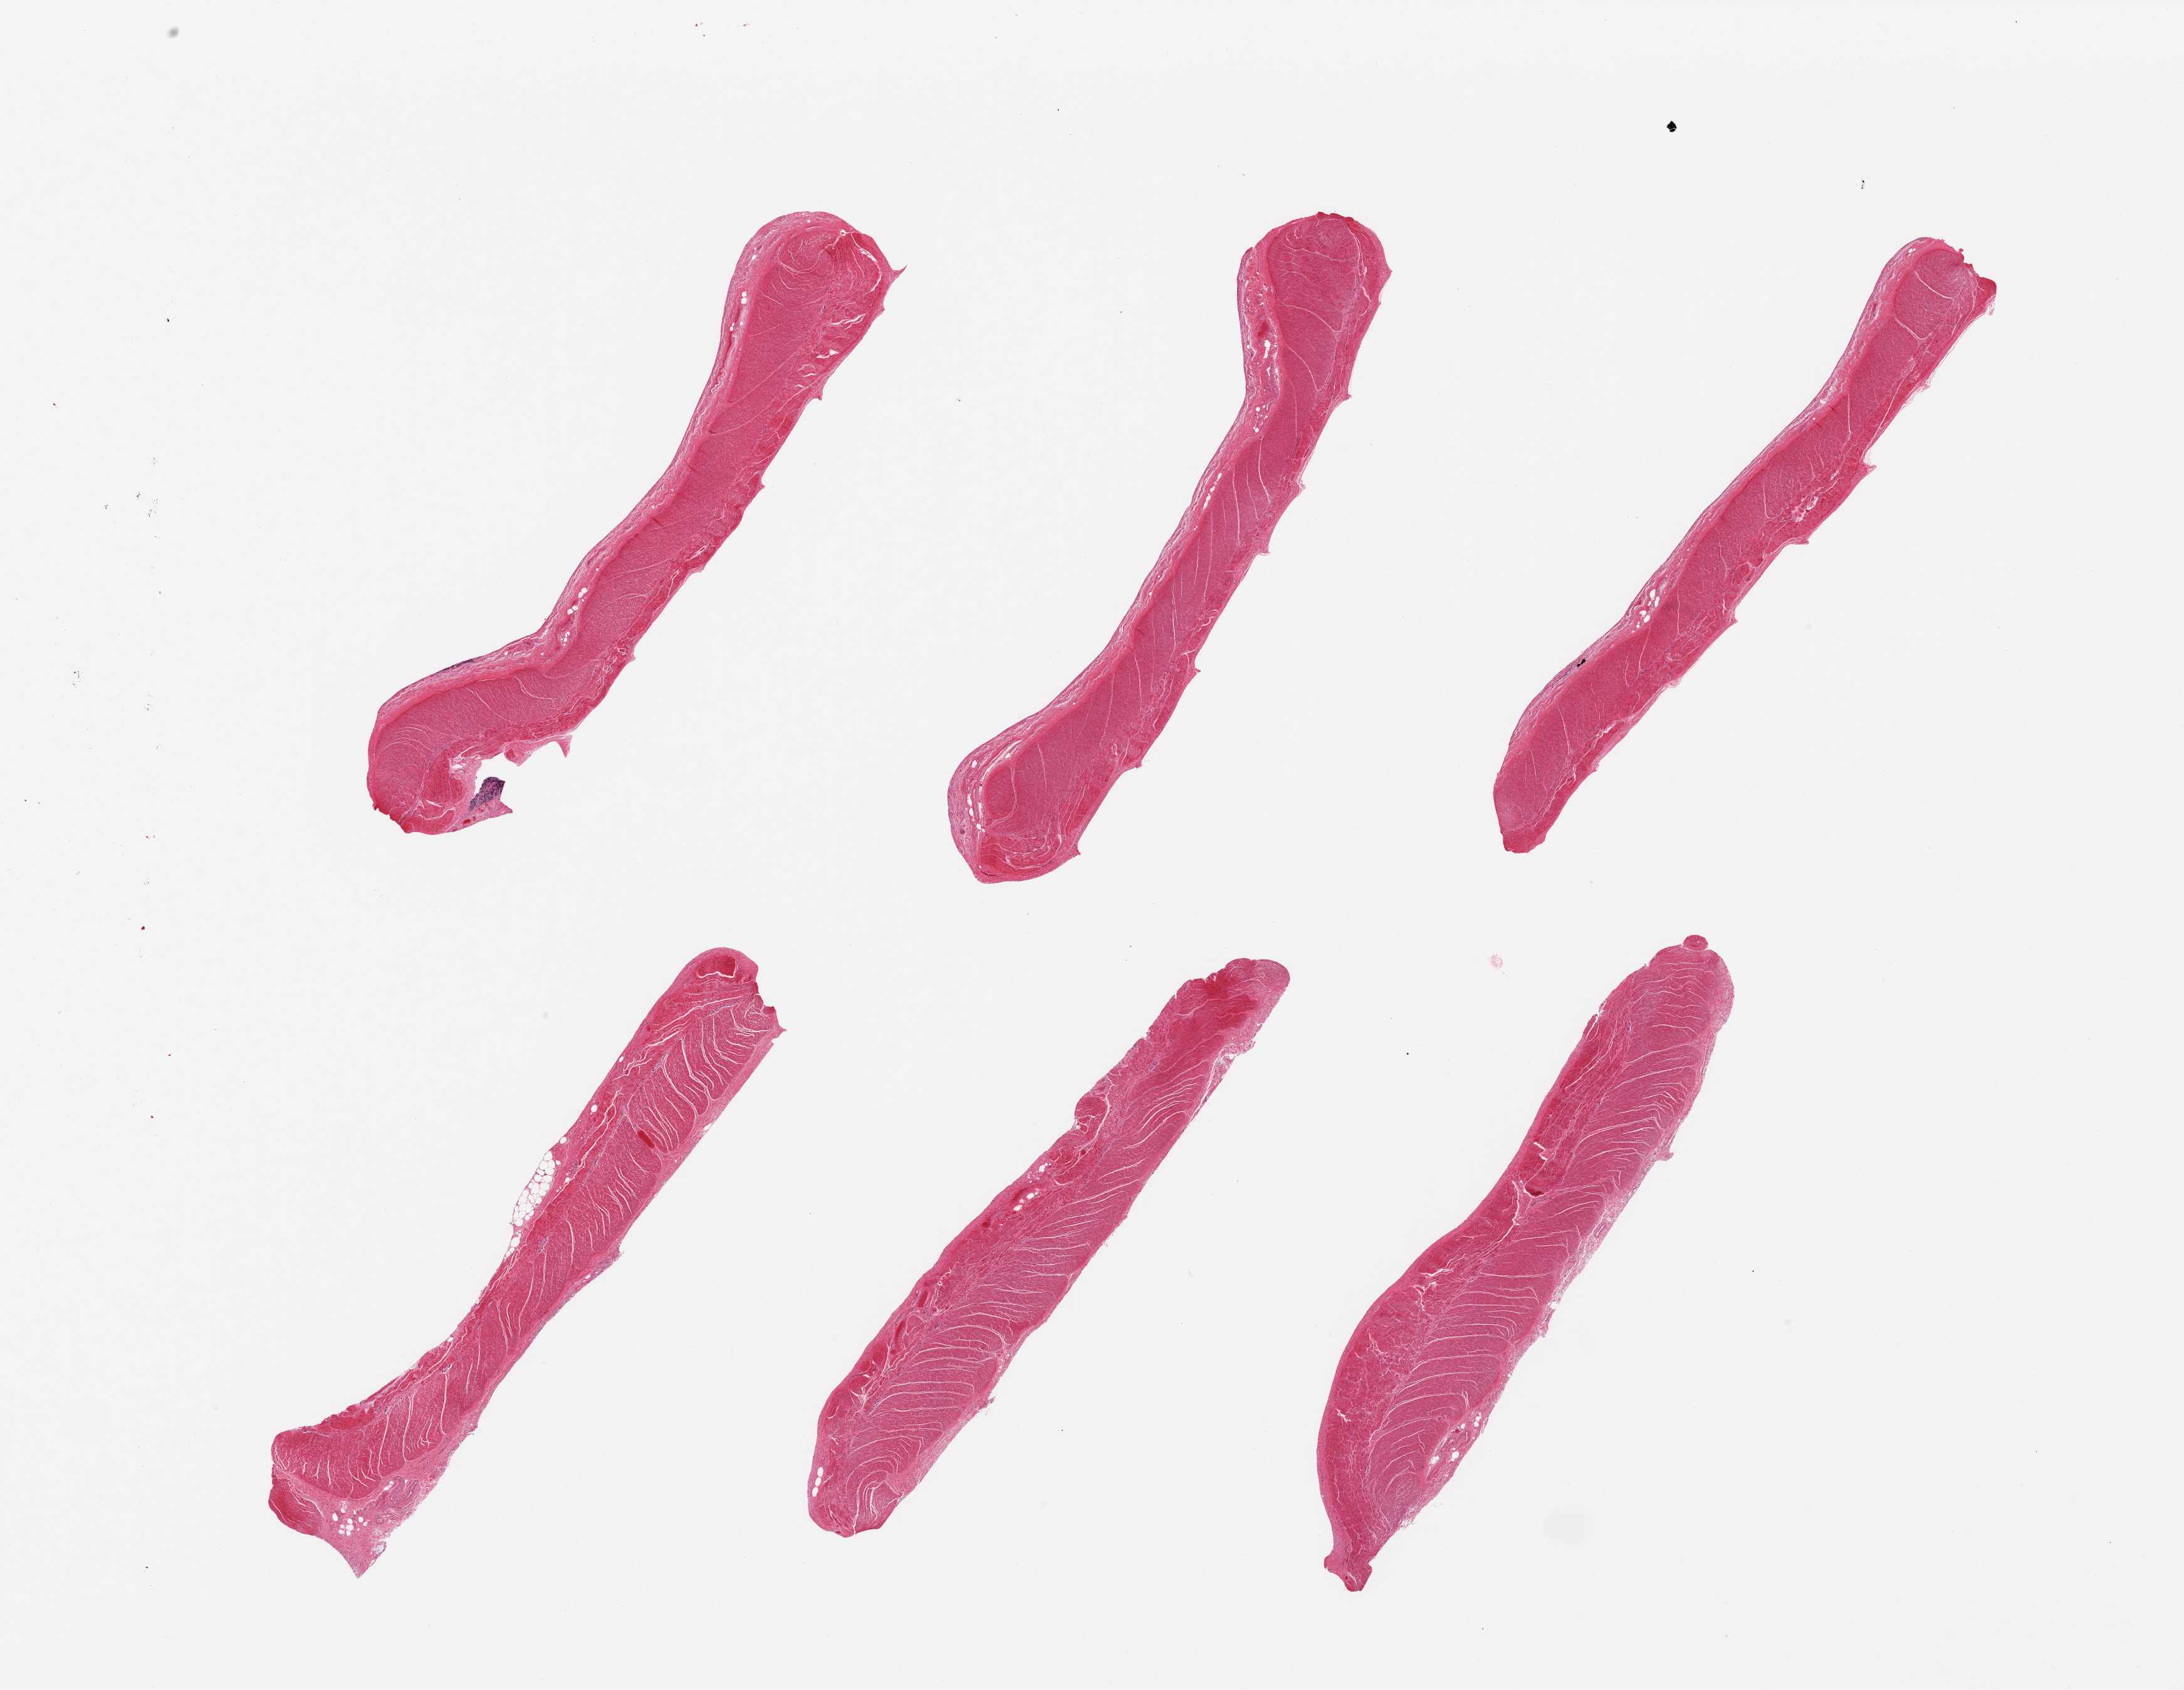
Digitized H&E-stained section — whole scanned area (about 27.6 x 21.3 mm, from a 20x scan) shown as a low-resolution overview, PAXgene-fixed paraffin-embedded (PFPE) section, target tissue: sigmoid colon, tissue donor sample. Donor: male.
Pathologist's review note for this sample: 6 pieces; target muscularis.